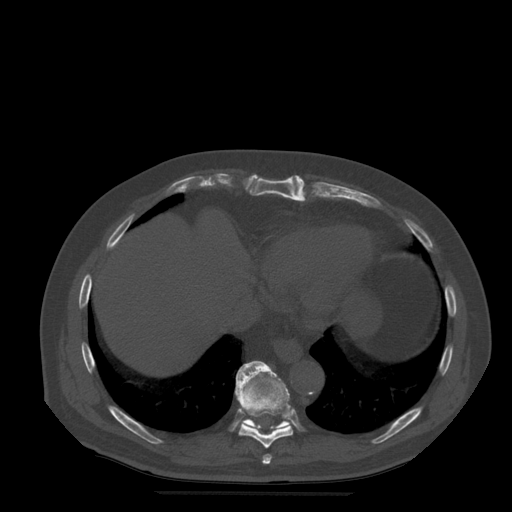
CT including the spine, one axial slice; slice 284 of 522 in the series (ordered by position); bone window (W 1800 / L 400 HU); 512 × 512 image matrix, field of view 420 × 420 mm. Patient age 72 years. Case-level facts recorded for this patient, not image findings: primary cancer: prostate.
Annotated regions visible in this slice (semi-automatic segmentation, software-assisted and operator-edited):
- T10 vertebra: bounding box <237,361,289,431> (left, top, right, bottom; pixels)
- T8 vertebra: <262,454,272,465>
- T9 vertebra: <235,363,294,449>